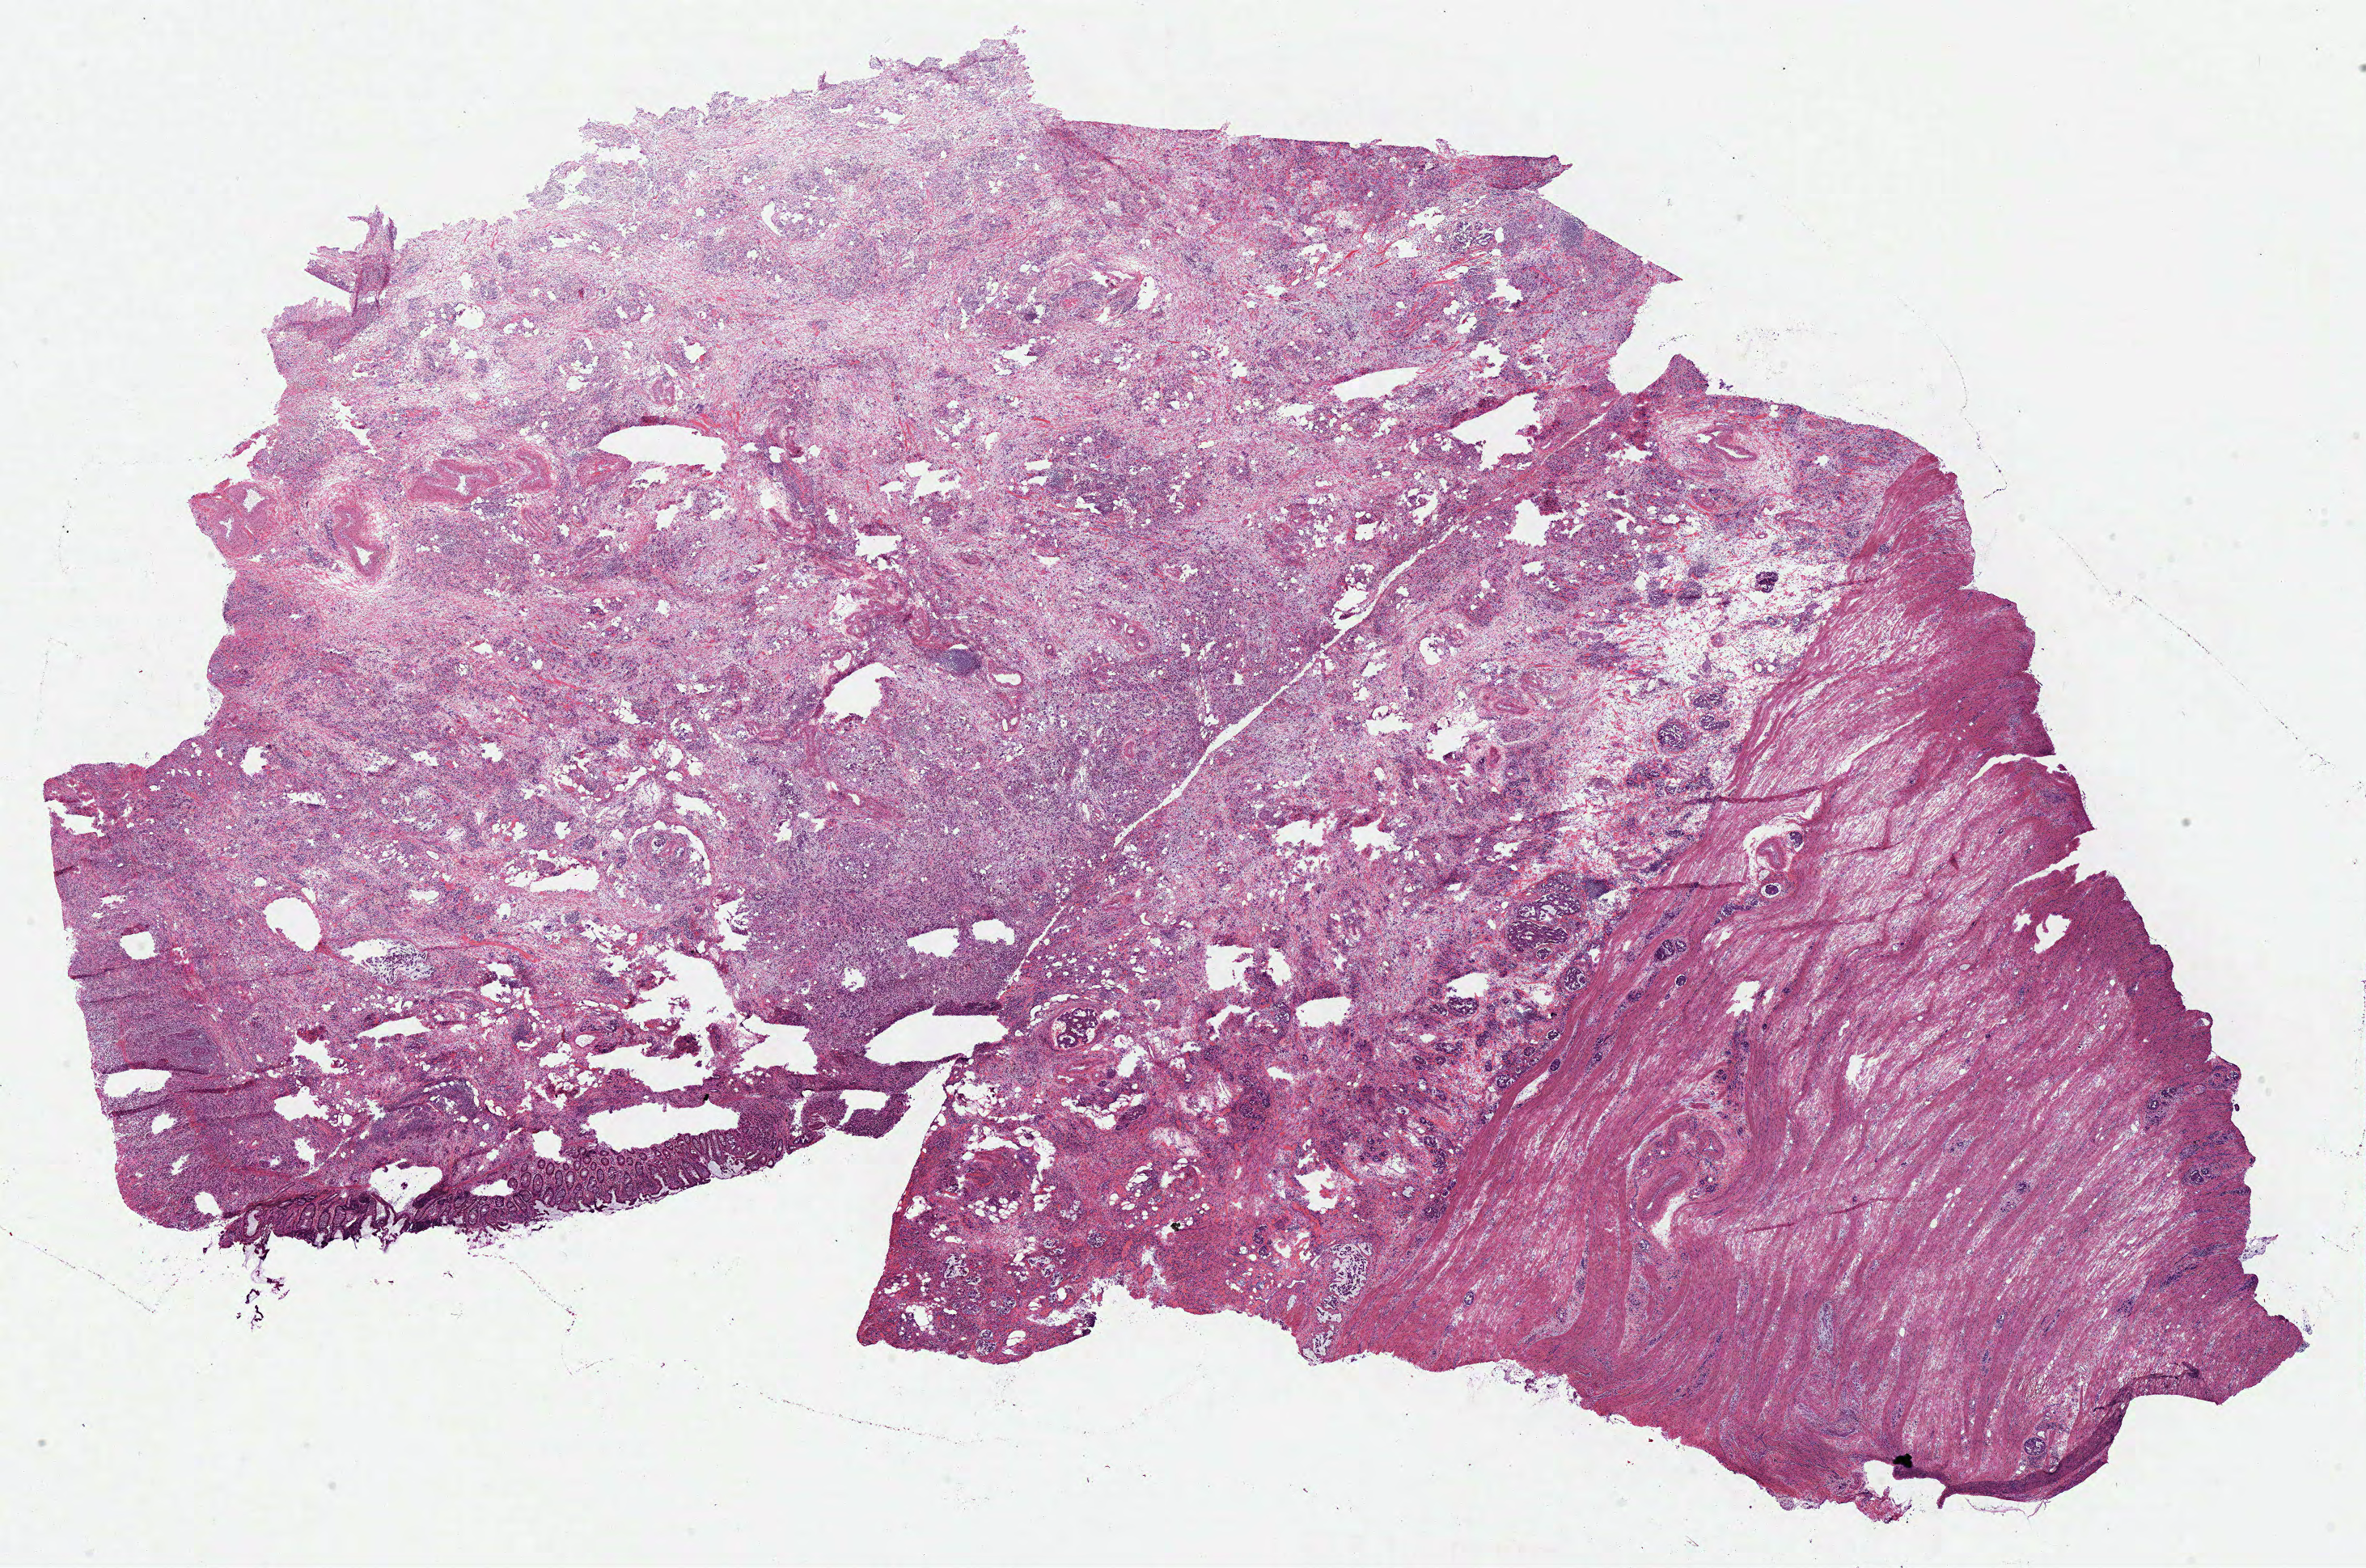
Digitized H&E tissue section (whole slide), a low-resolution overview of the entire scanned area, about 23.0 x 15.2 mm, frozen section from the bottom of the tissue portion, sample: primary tumour, colon. Female patient; age at initial diagnosis 57 years. Slide review estimates, as recorded: tumour cells 51%, tumour nuclei 65%, normal cells 3%, stromal cells 45%, necrosis 1%.
TNM: T3 N2b M0. Pathologic diagnosis: Adenocarcinoma, NOS. AJCC pathologic stage: IIIC (7th edition).